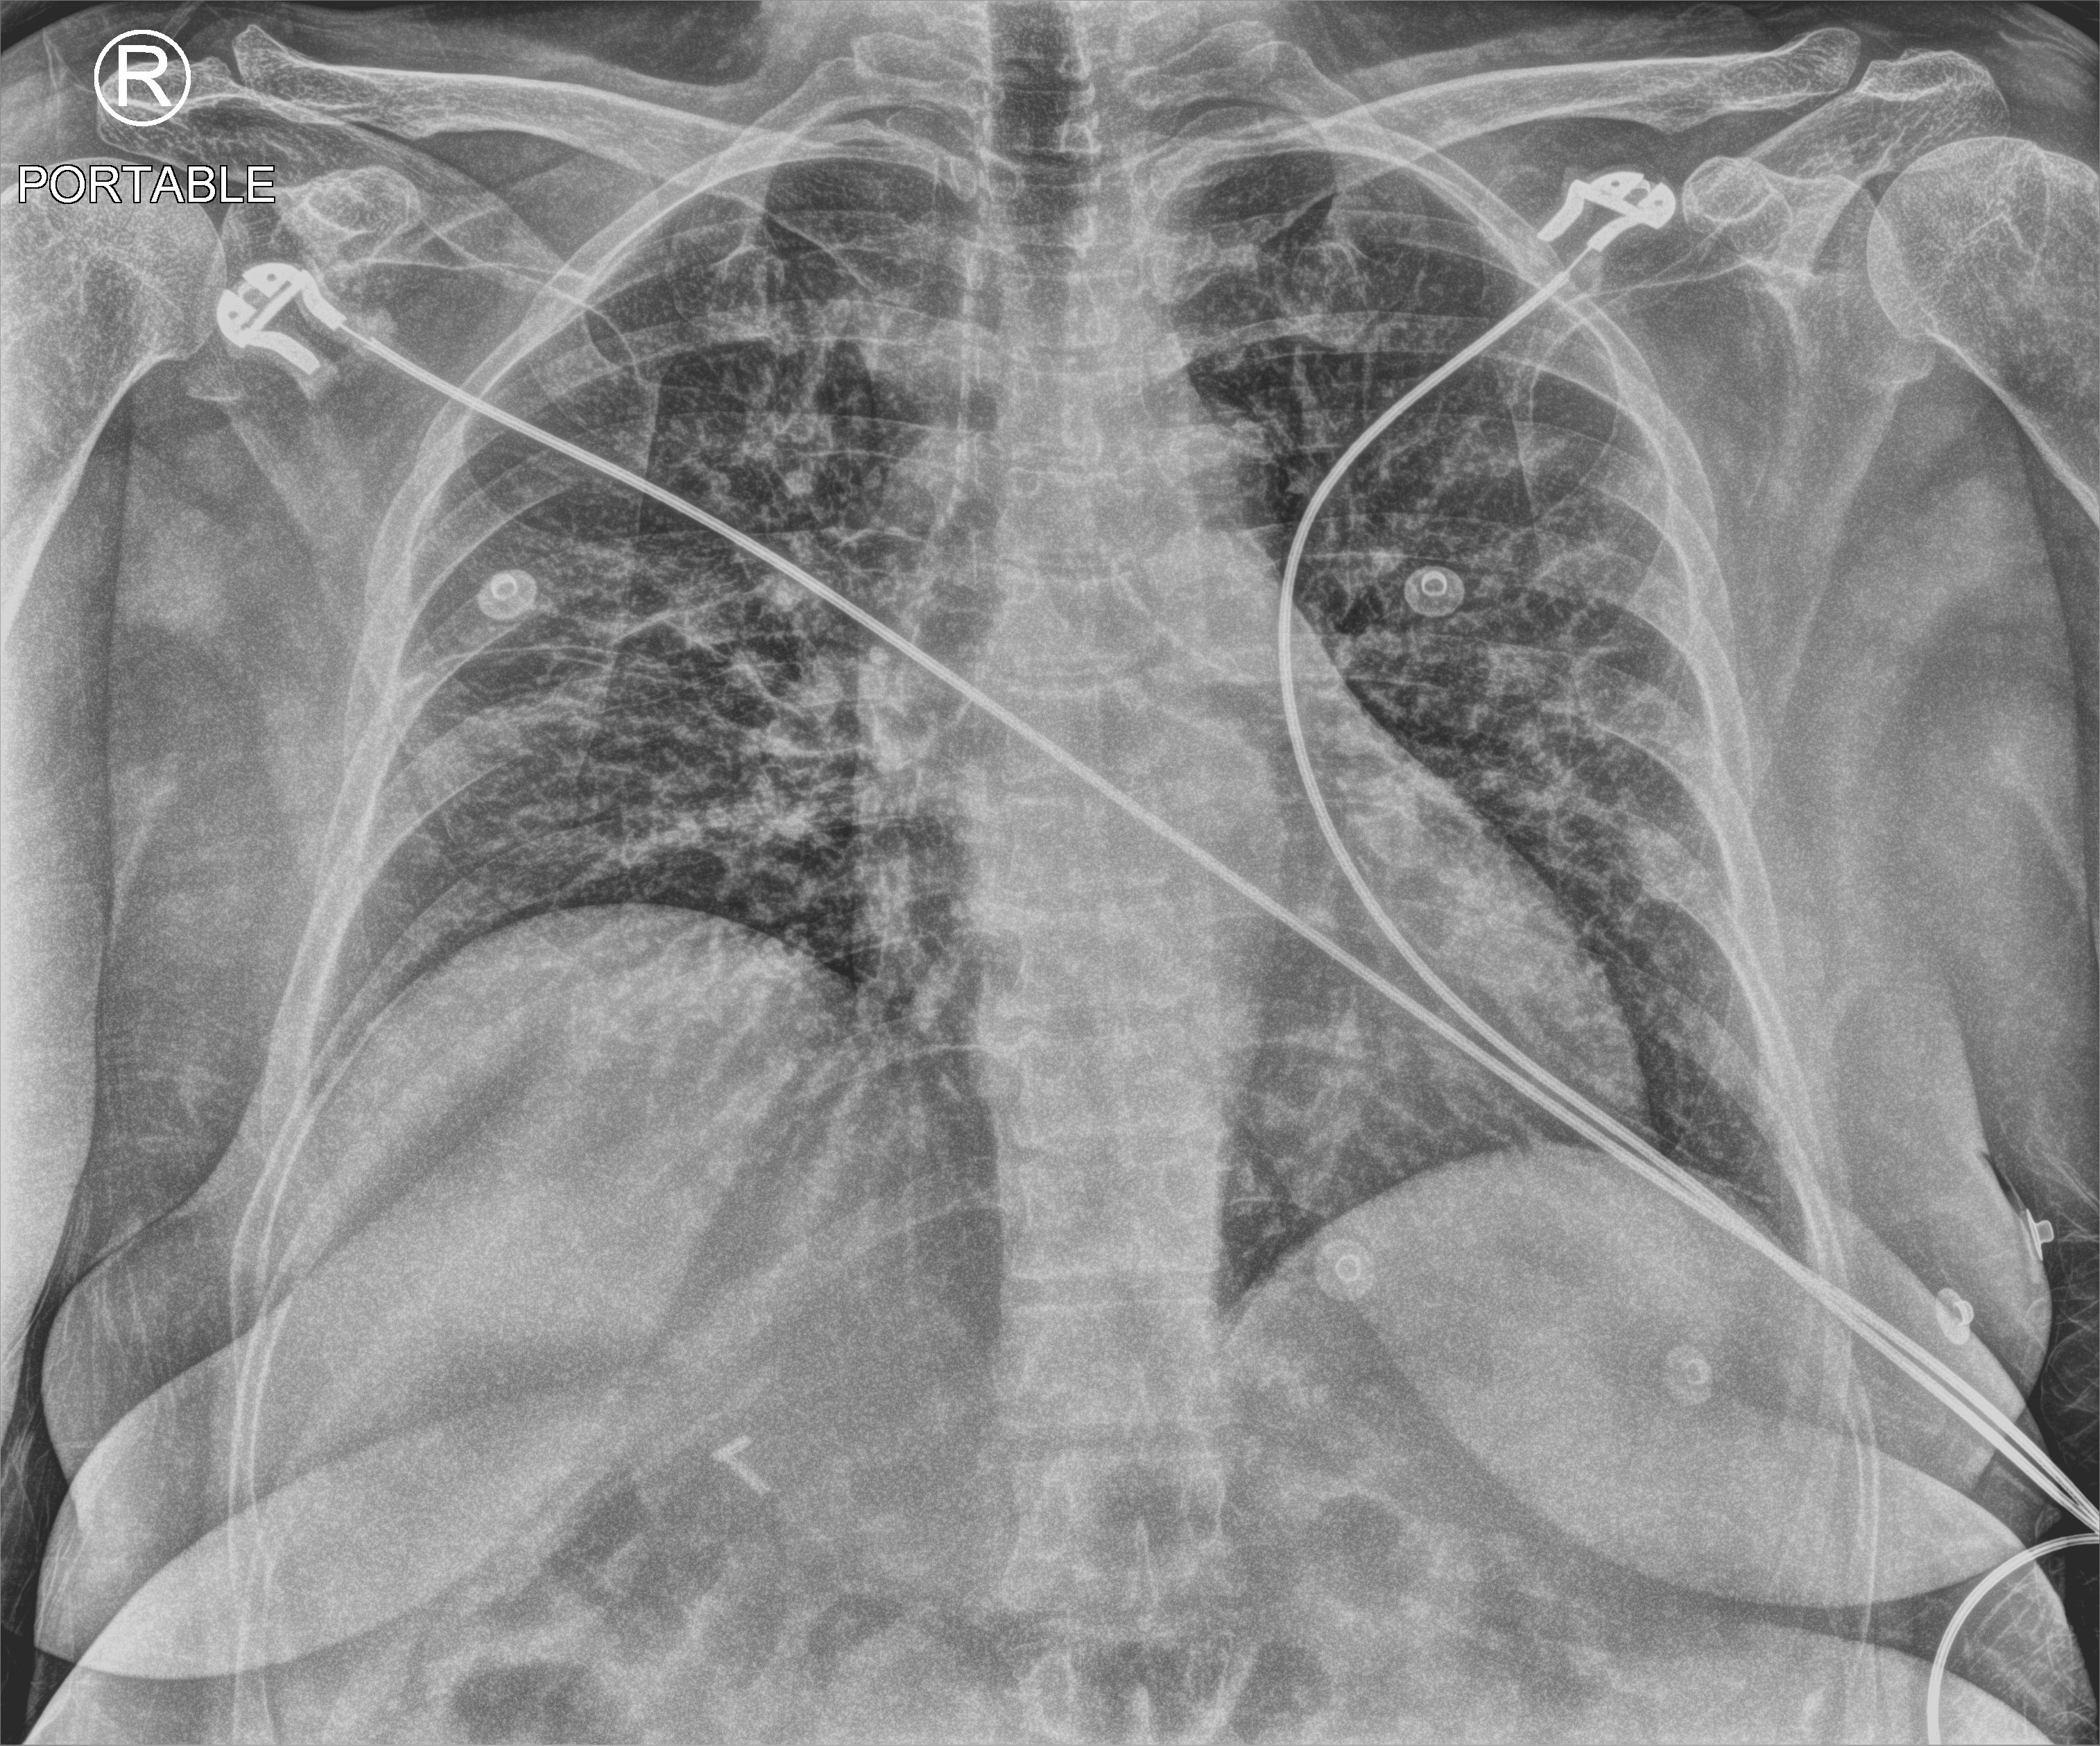
Chest X-ray (portable); anteroposterior (AP) projection. Patient hospitalised with COVID-19; female, aged 18–59 years.
Admission-level facts for this patient (not findings on this image; timing relative to this image not recorded): COPD (admission record): no; admitted to intensive care during this hospital stay: yes; mechanically ventilated during this hospital stay: yes.